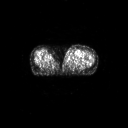
FDG PET of an extremity soft-tissue mass (from a PET/CT study), one axial slice; position 49 of 91 along the scan axis; 3.27 mm slice thickness; 128 × 128 image matrix, field of view 700 × 700 mm. Patient: female, 74 years. Case-level facts recorded for this patient, not image findings: histological type: pleomorphic leiomyosarcoma; grade: high; site of the primary tumour: left thigh.
Outlined on this slice (expert contour drawn on MRI and transferred to this co-registered scan by the dataset authors):
- gross tumour volume including surrounding oedema: bounding box (x1, y1, x2, y2) in pixels: (65, 50, 77, 61)